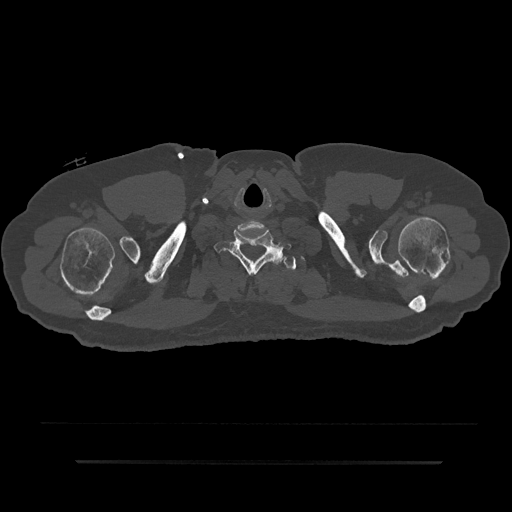
CT including the spine, one axial slice; slice 770 of 797 in the series (ordered by position); 120 kVp; bone window (W 1800 / L 400 HU); 0.5 mm slice thickness; 512 × 512 image matrix, field of view 464 × 464 mm. Patient: male, 59 years. From the clinical record (not read from this slice): primary cancer: bile ducts; vertebrae with lytic lesions (as recorded): T10.
Annotated regions visible in this slice (semi-automatically segmented with operator editing):
- T1 vertebra: box from (x=271, y=255) to (x=296, y=270) px